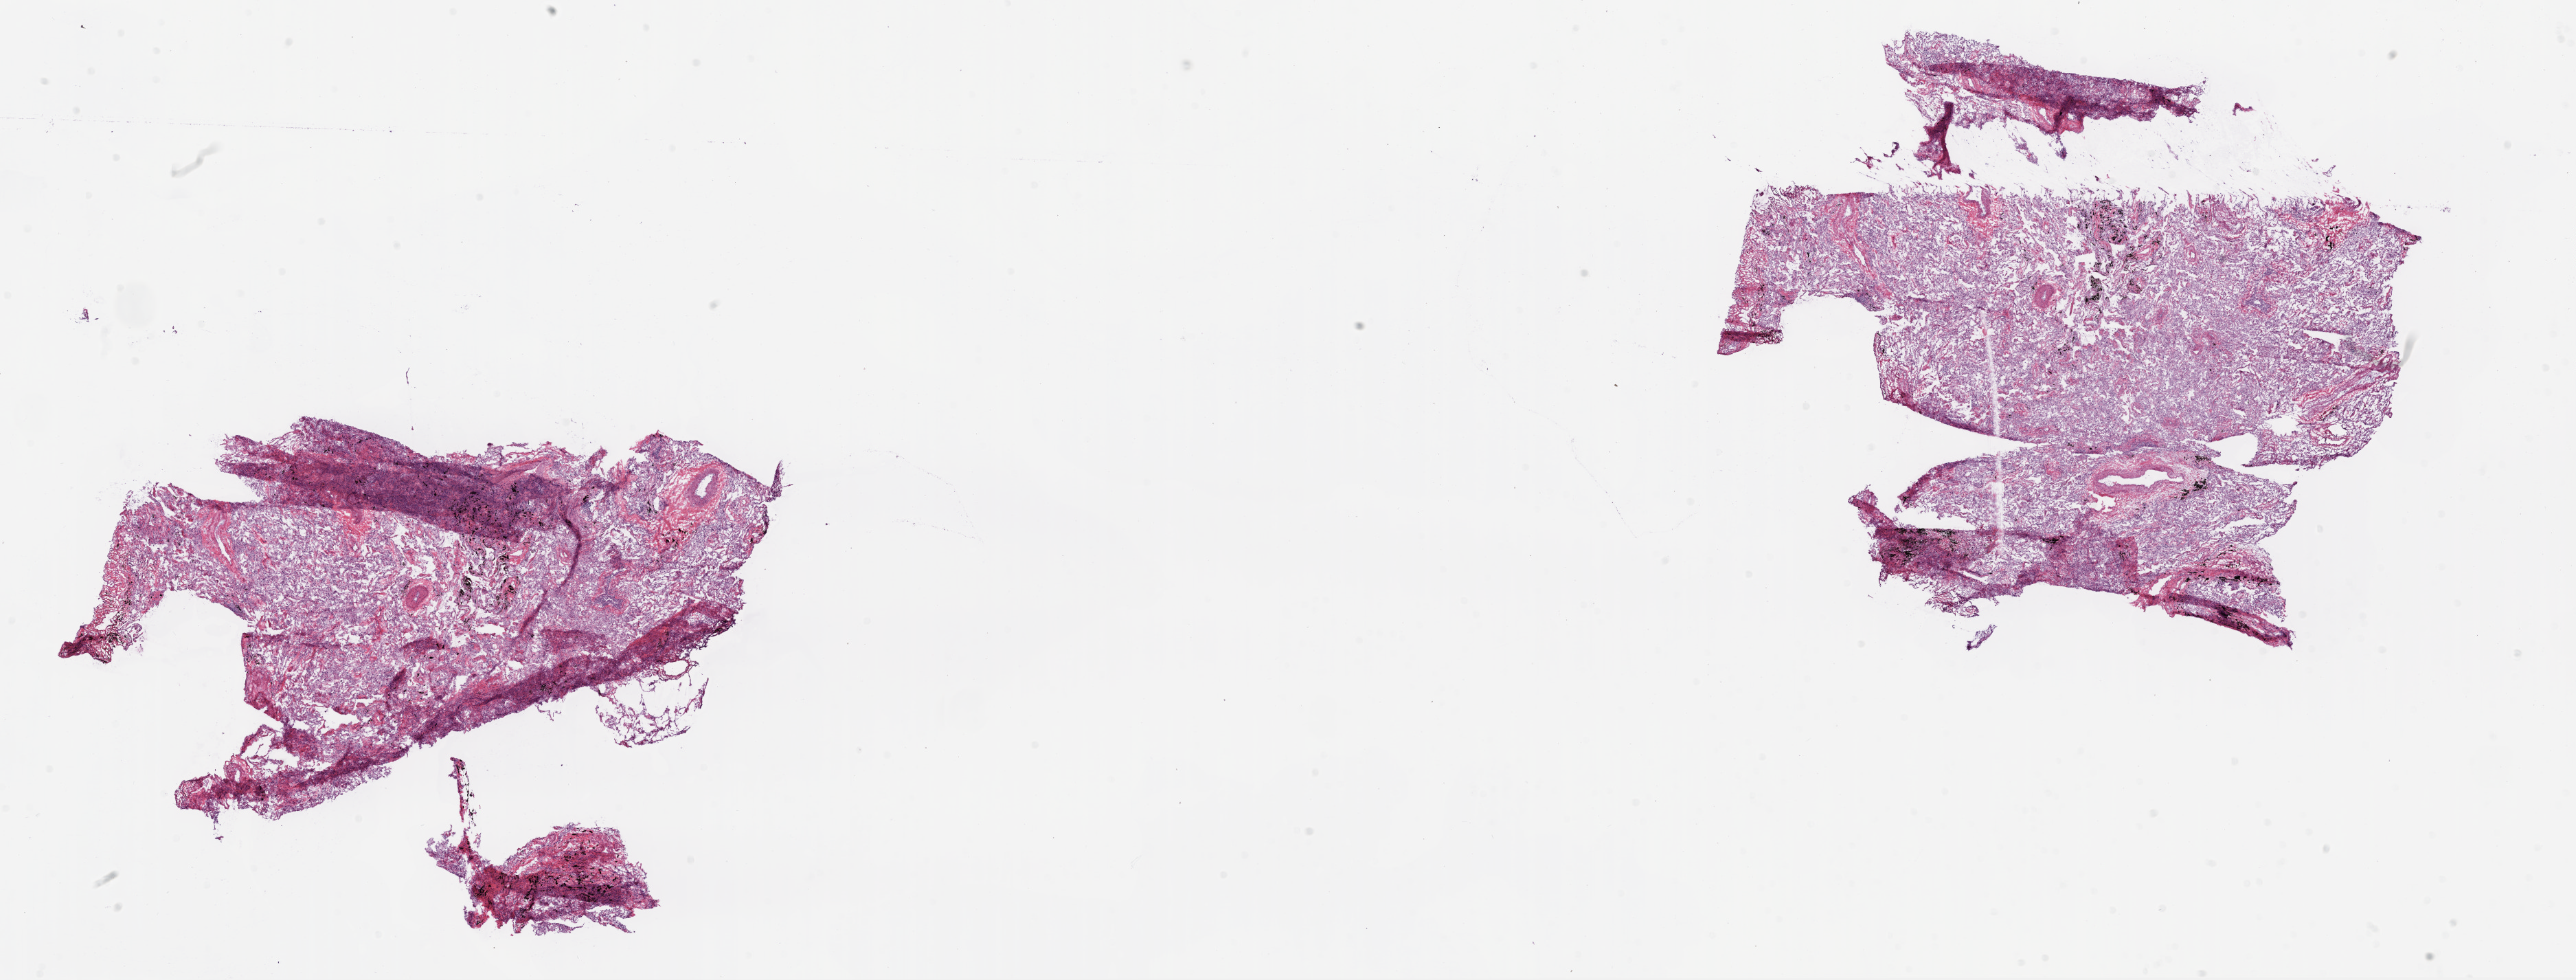
Digitized H&E-stained tissue section (whole slide) — shown as a low-resolution overview of the whole scanned area (about 30.1 x 11.4 mm). Frozen section from the bottom of the tissue portion. Lung, solid tissue normal (non-tumour tissue) sample. Male, age 72 years at initial diagnosis.
* this section: solid tissue normal (non-tumour) sample from the same patient
* patient diagnosis: Squamous cell carcinoma, NOS (upper lobe, lung)